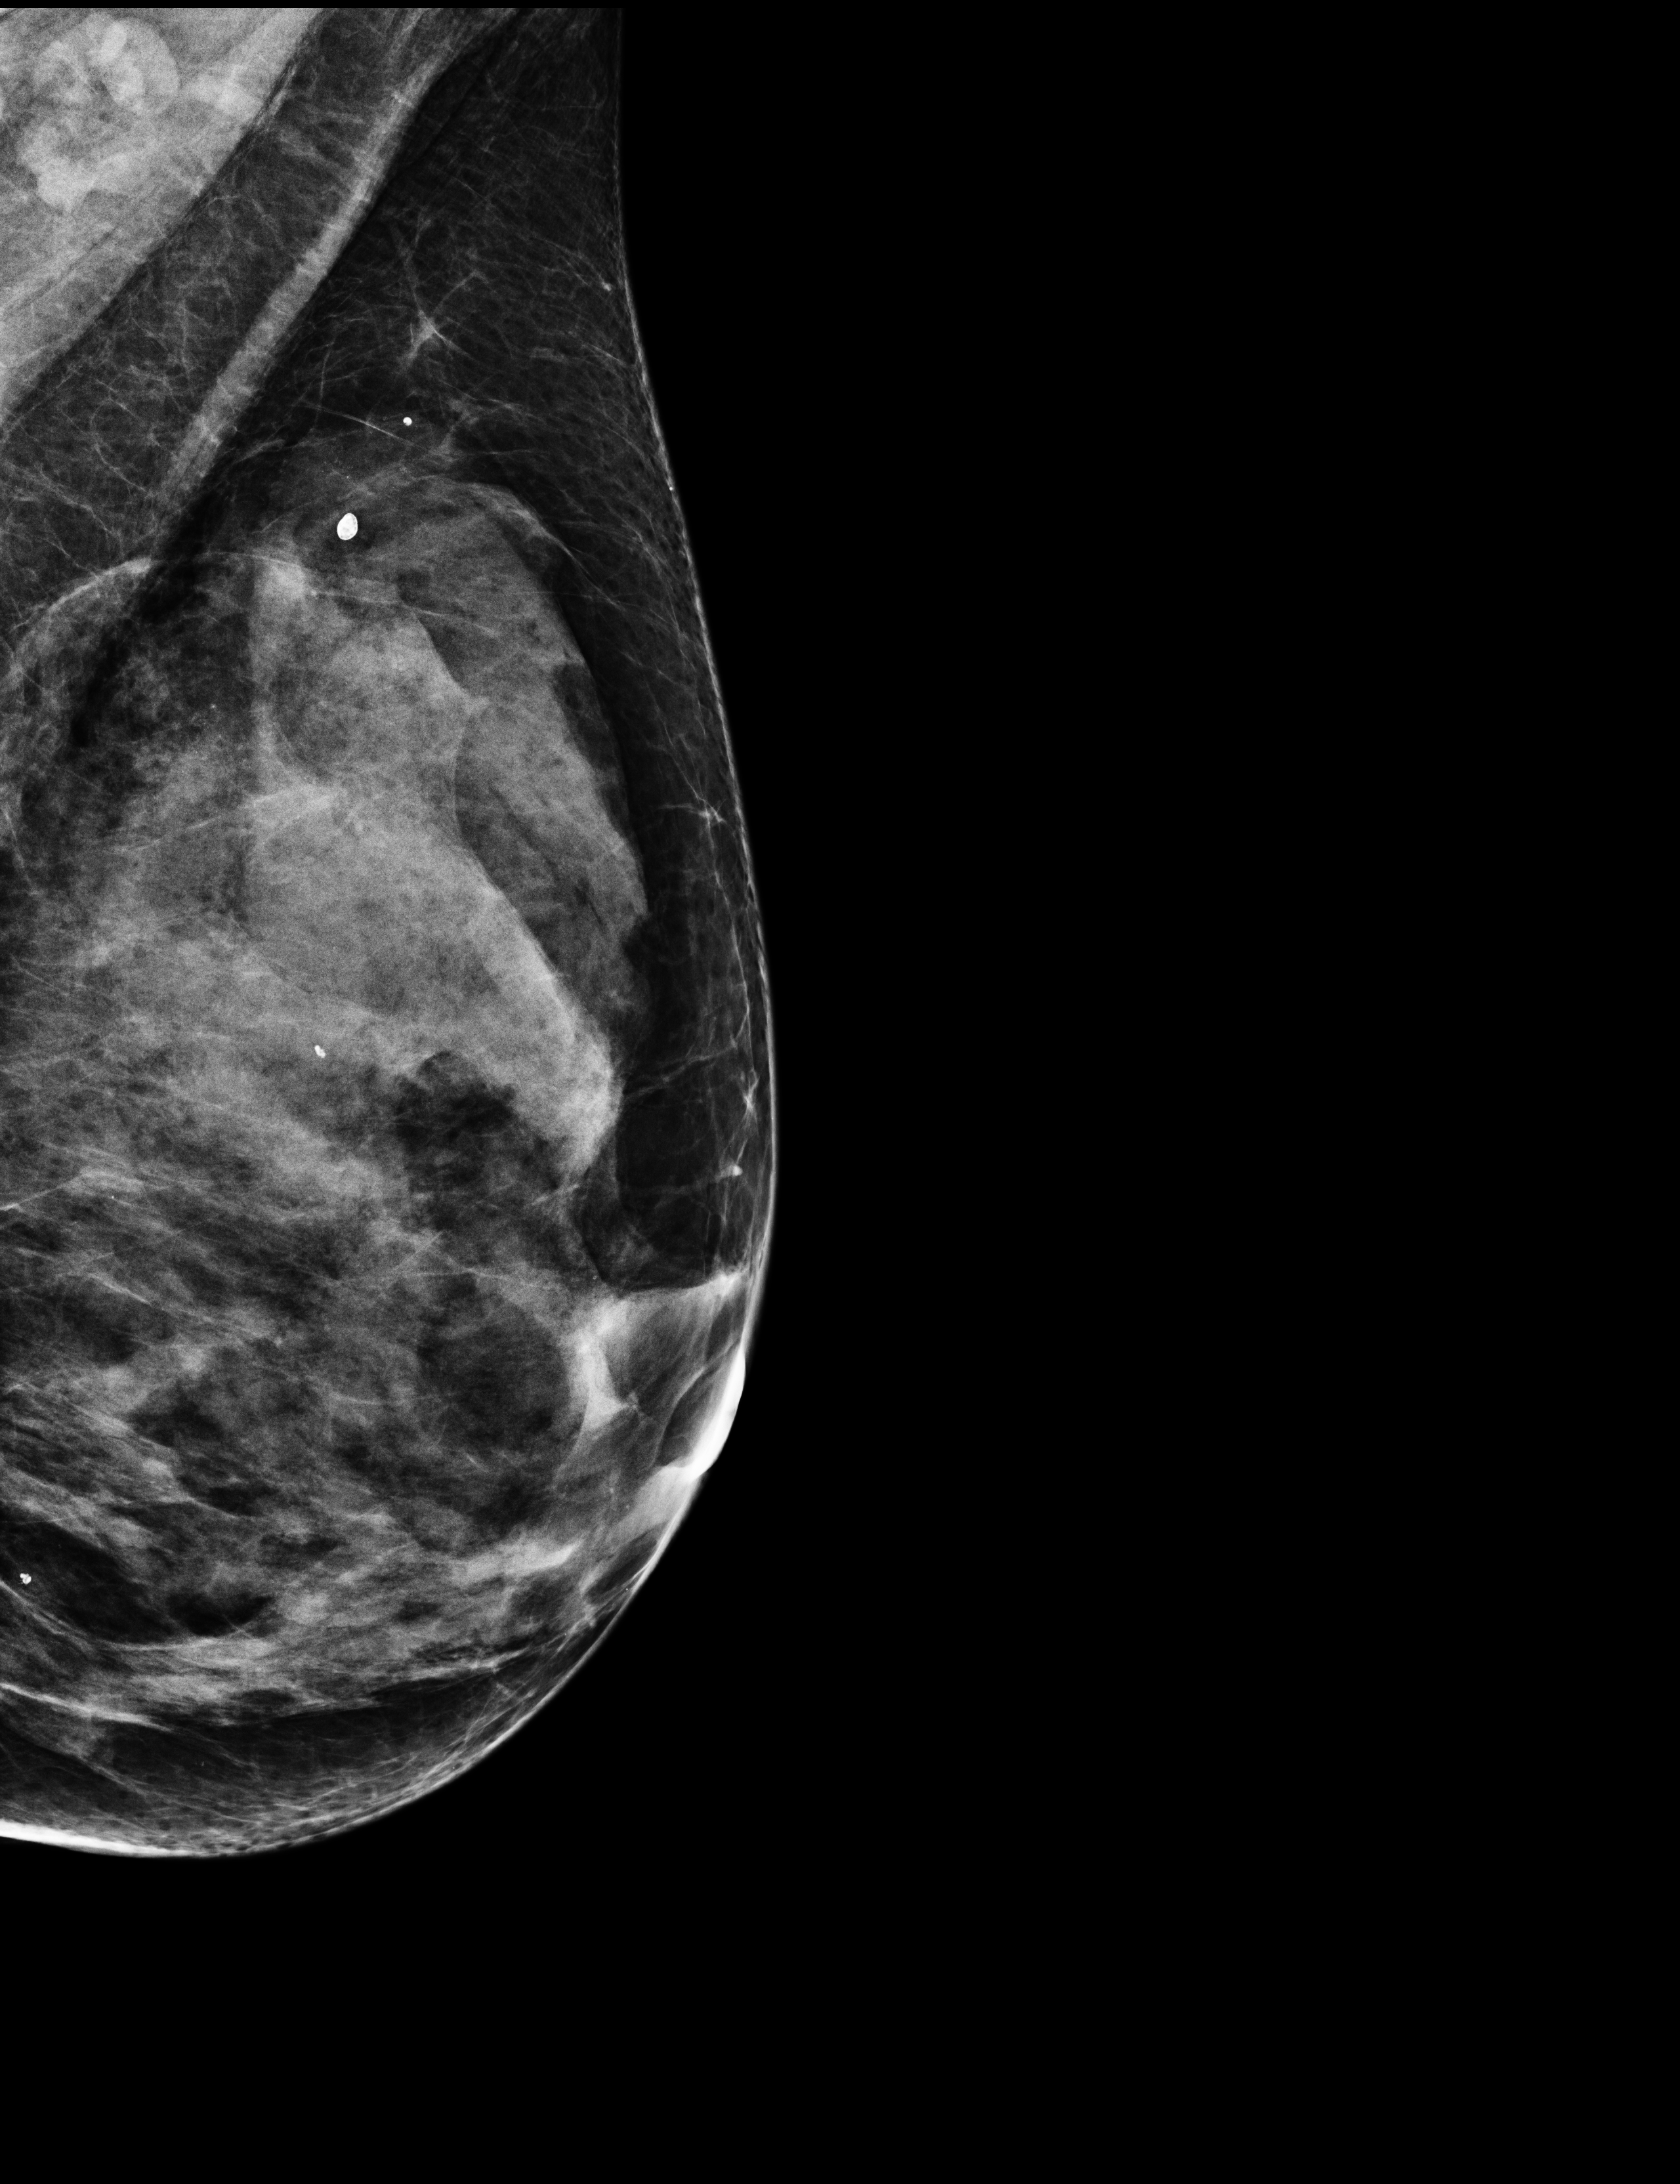
Annual screening mammography examination.
Image type: full-field digital mammogram. Breast: left. Projection: medio-lateral oblique projection.